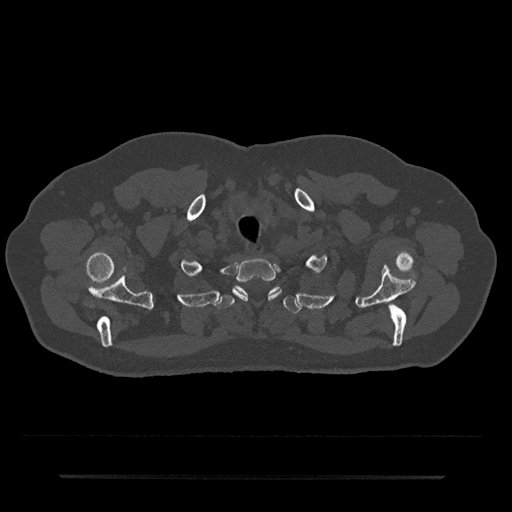
CT including the spine, one axial slice. Slice 627 of 797 in the series (ordered by position). Reconstruction kernel Br40s/3. 120 kVp. Bone window (W 1800 / L 400 HU). 0.5 mm slice thickness. 512 × 512 image matrix. Male patient, age 69 years. From the clinical record (not read from this slice): primary cancer: prostate.
Structures marked on this image (semi-automatically segmented with operator editing):
- T1 vertebra: bounding box [x1, y1, x2, y2] px = [233, 258, 282, 300]
- T2 vertebra: [216, 286, 301, 313]